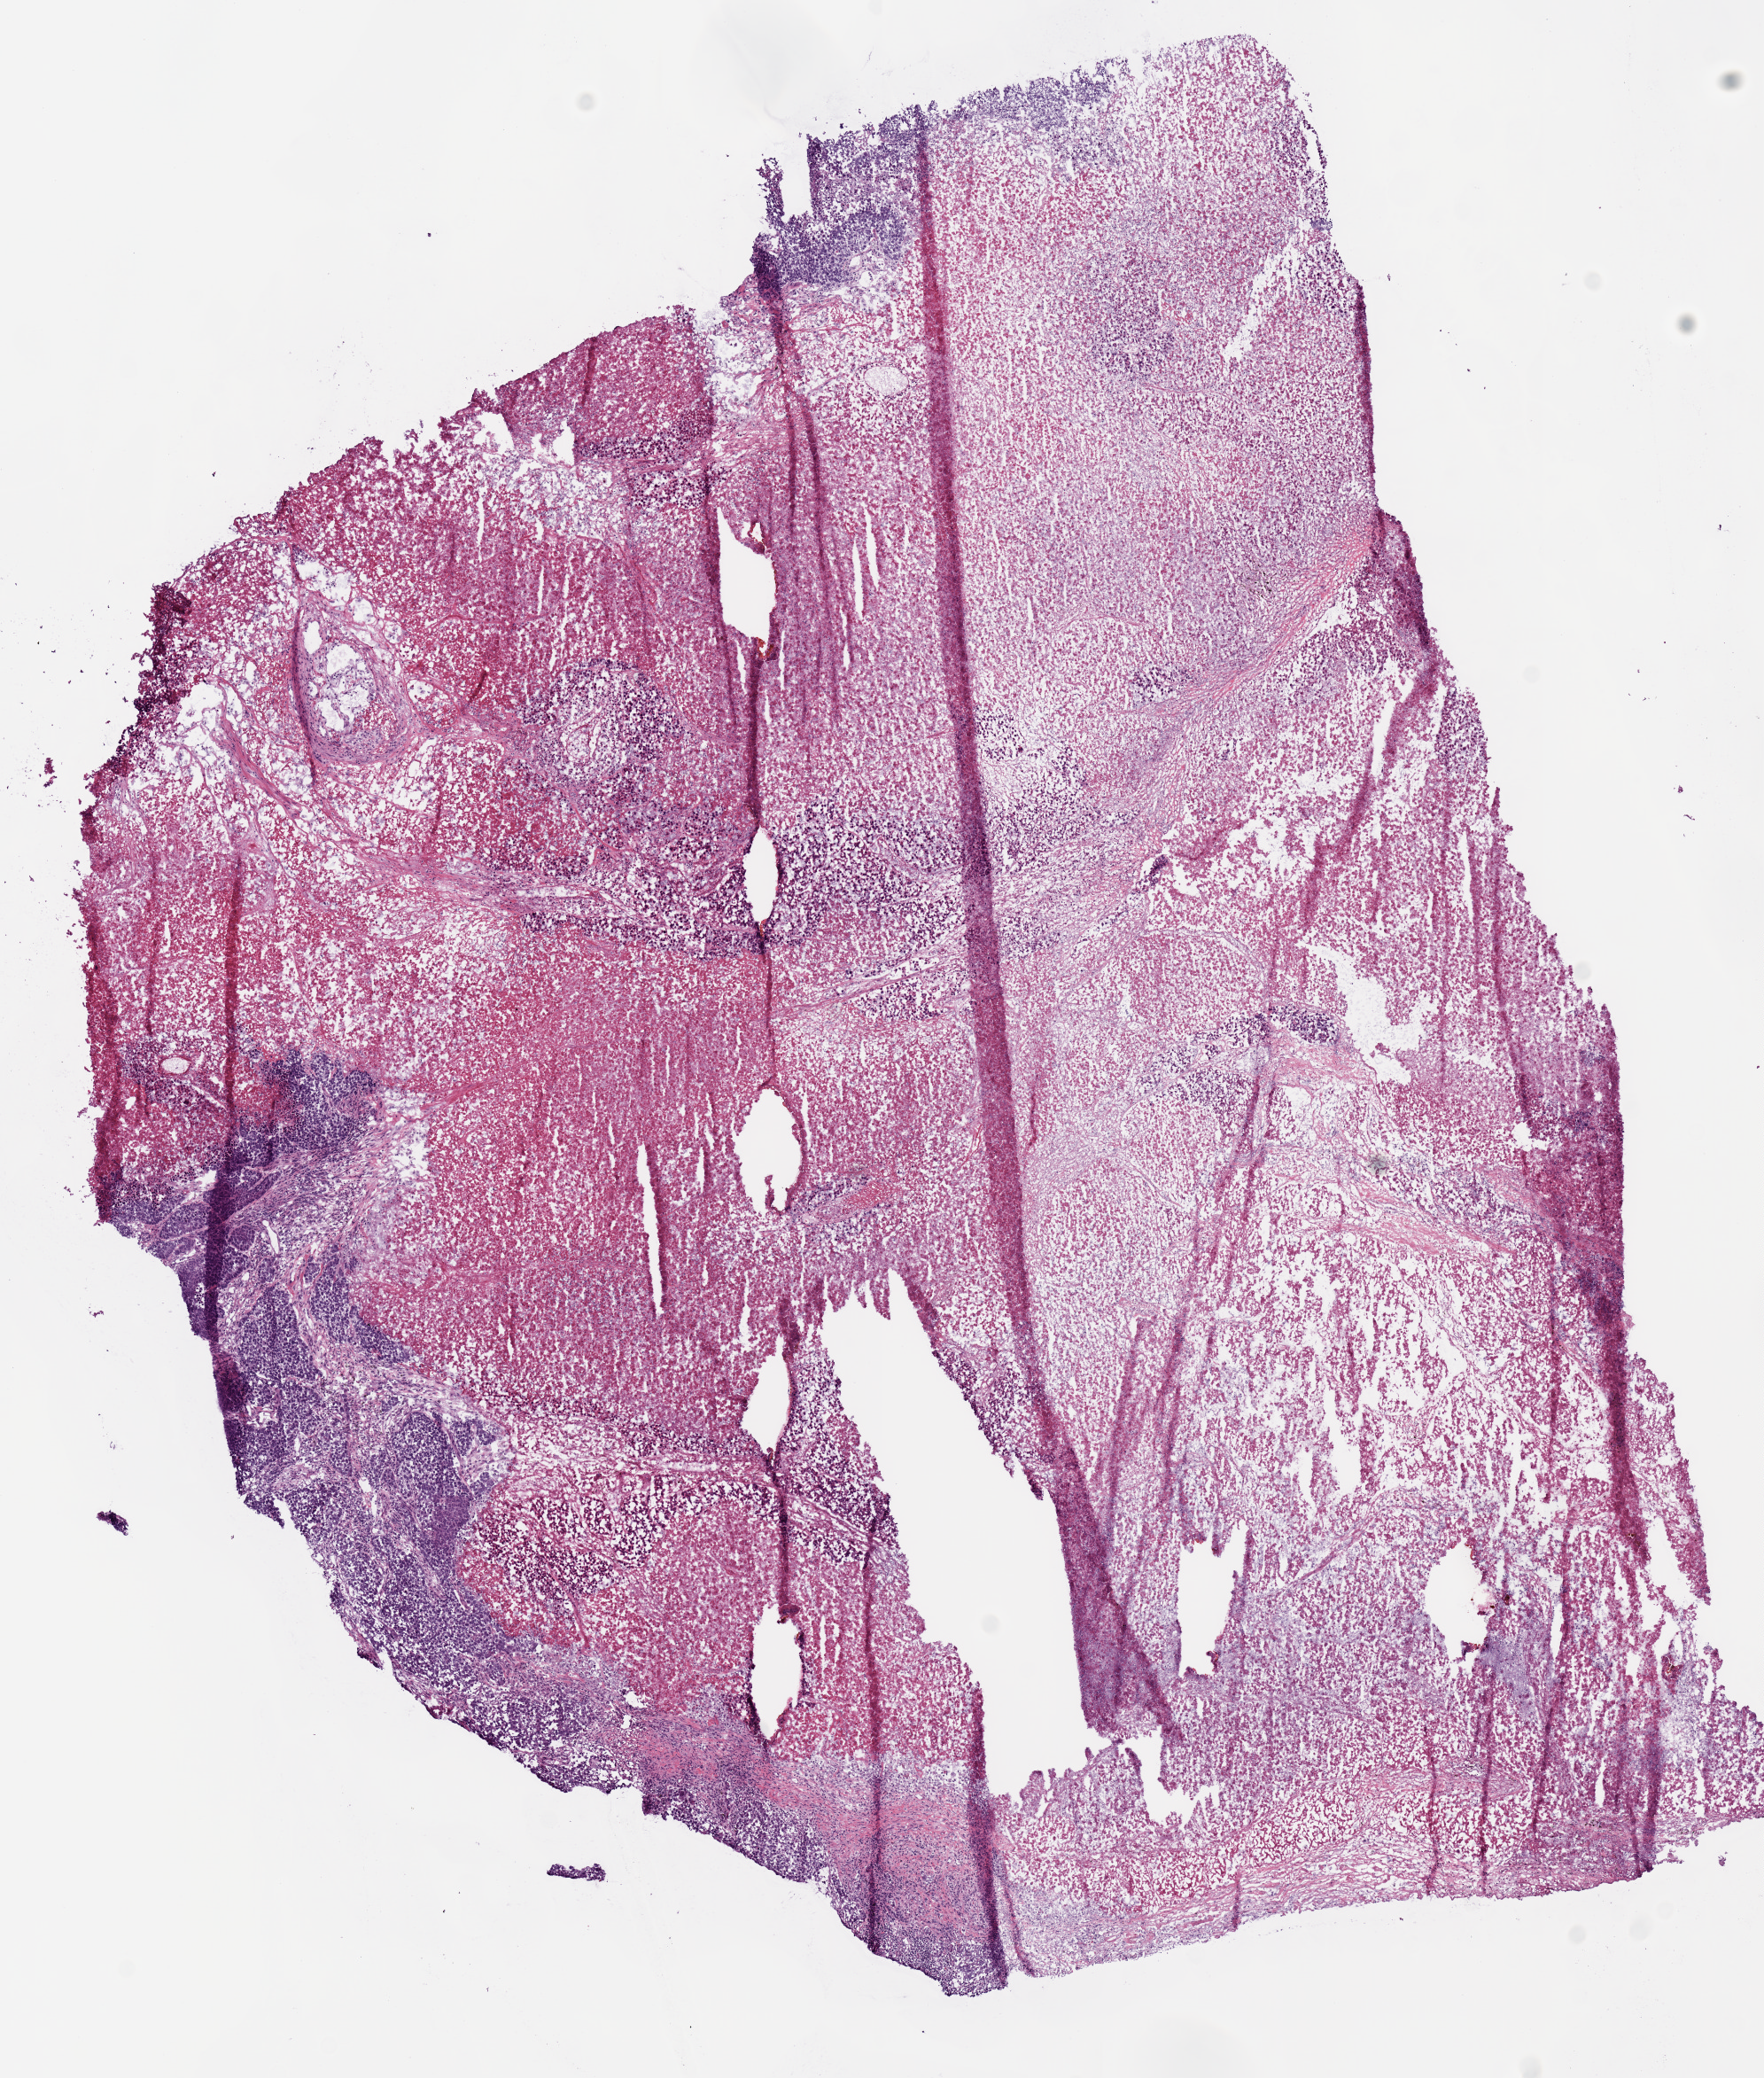
Whole-slide histology image, H&E — shown as a low-resolution overview of the whole scanned area (about 7.9 x 9.3 mm), frozen section, primary tumour sample from the lung. Female, age 49 years at initial diagnosis. Composition of this section per pathologist review: tumour cells 85%, tumour nuclei 80%, normal cells 0%, stromal cells 10%, necrosis 5%.
* AJCC pathologic stage: IIB
* histologic diagnosis: Adenocarcinoma, NOS
* TNM: T3 N0 MX